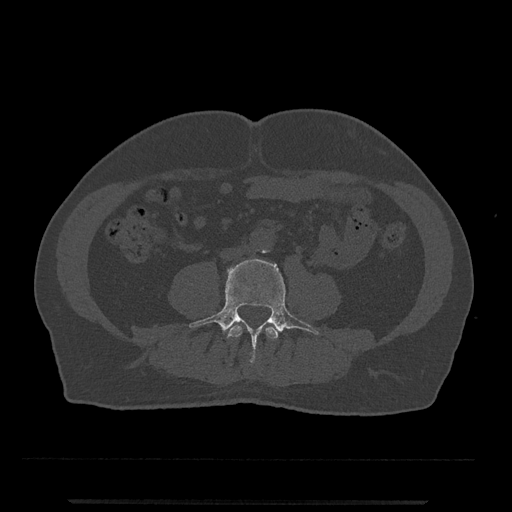
CT including the spine, one axial slice. 120 kVp. Bone window (W 1800 / L 400 HU). 0.5 mm slice thickness. 512 × 512 image matrix, field of view 419 × 419 mm. Patient: male, 63 years. Case-level facts recorded for this patient, not image findings: primary cancer: prostate.
Outlined on this slice (semi-automatic segmentation, software-assisted and operator-edited):
- L3 vertebra: box from (x=227, y=324) to (x=278, y=366) px
- L4 vertebra: (x=189, y=259)–(x=320, y=365)